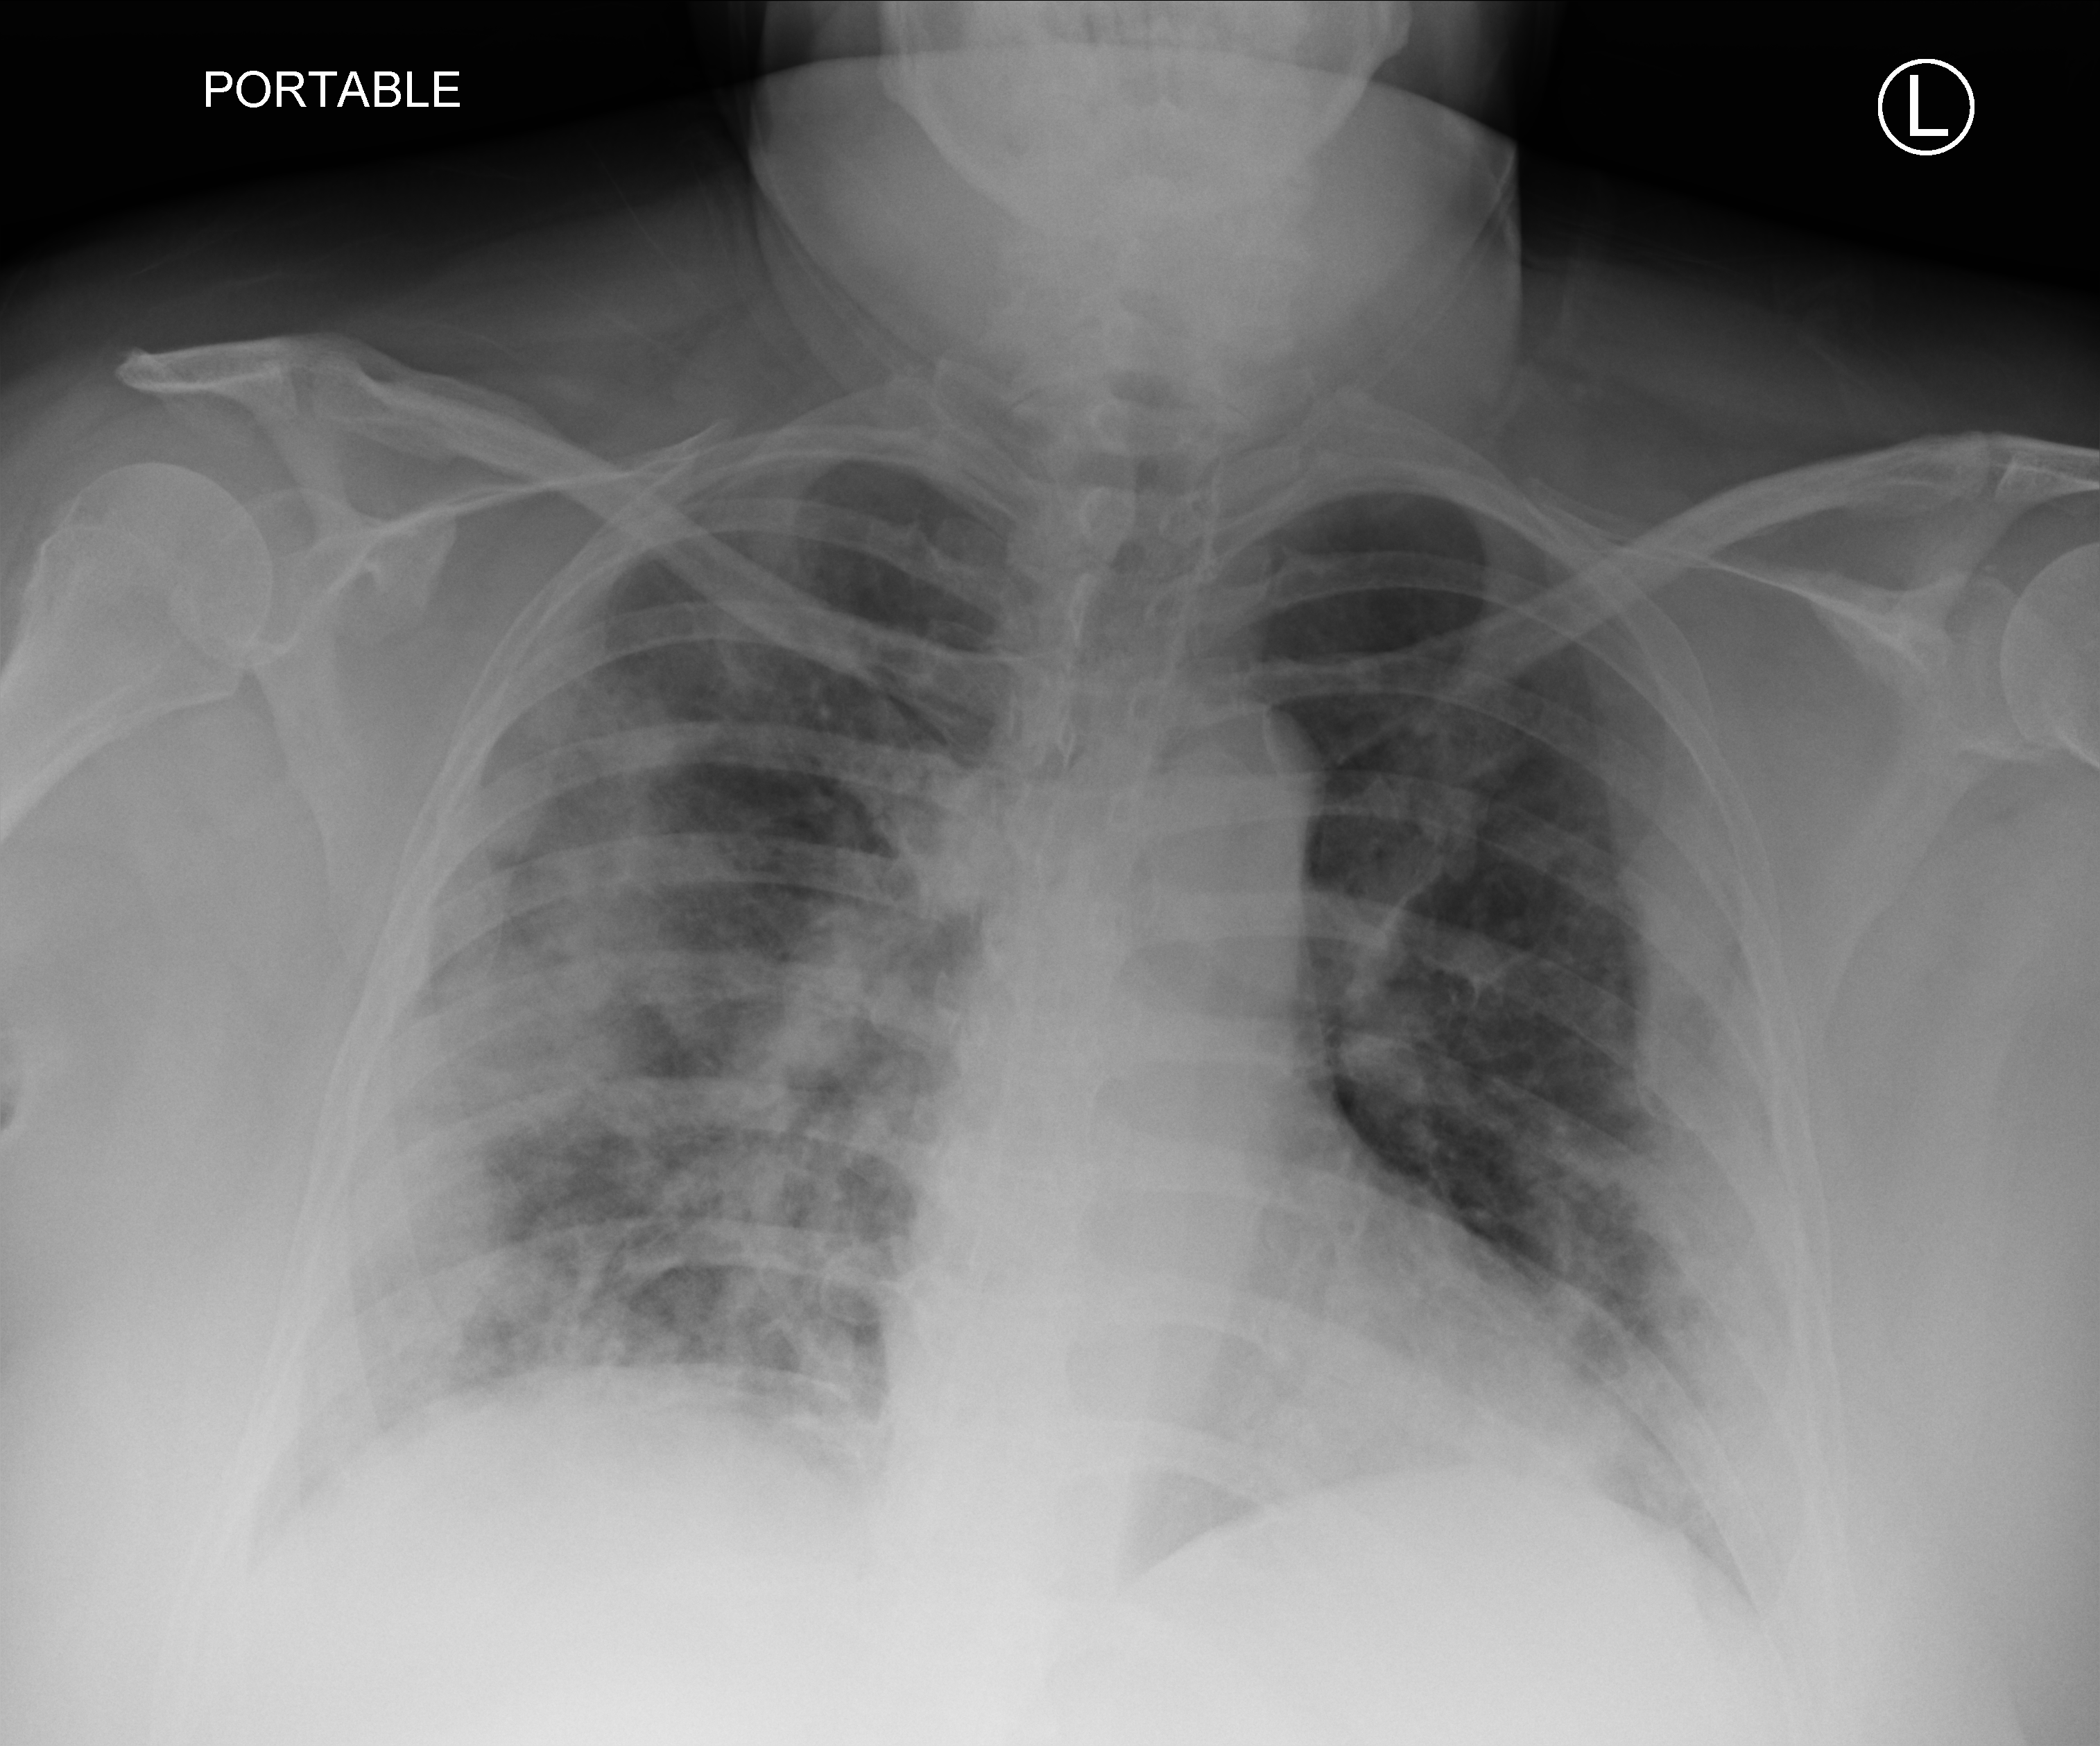
Chest X-ray (portable); anteroposterior (AP) projection. Female patient hospitalised with COVID-19, age 18–59 years.
From the hospital-stay record, not from the radiograph (when in the stay this image was taken is not recorded): admitted to intensive care during this hospital stay: no; length of hospital stay: 16 days; mechanically ventilated during this hospital stay: no.